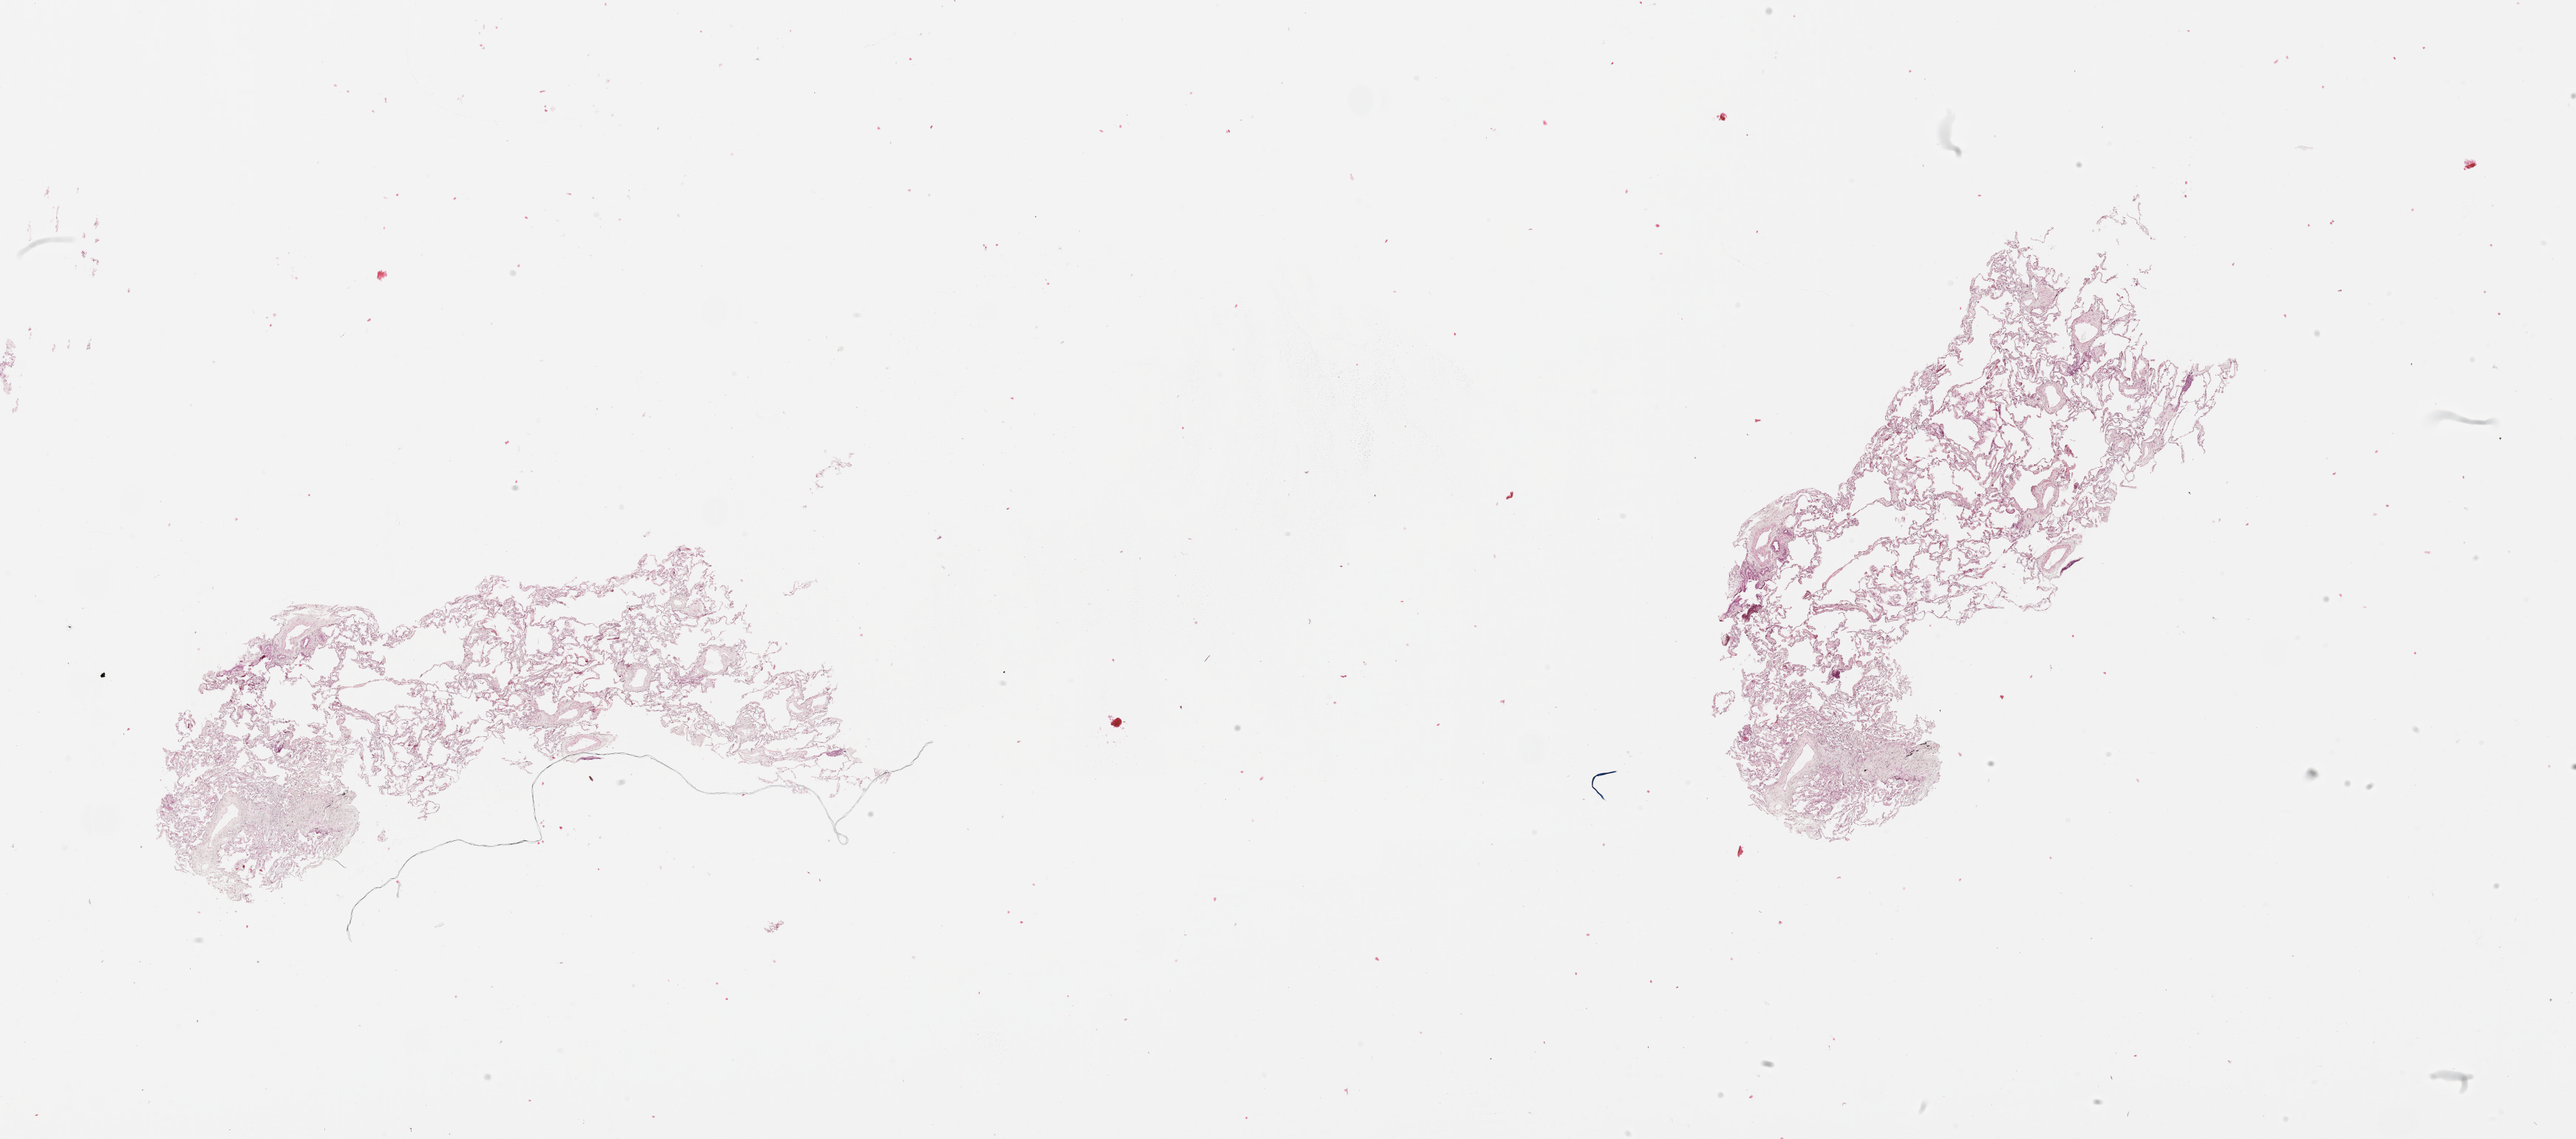
Digitized H&E tissue section (whole slide) — low-resolution overview of the scanned area, about 28.1 x 12.4 mm (from a 20x scan); lung, normal (non-tumour) tissue. 74-year-old female patient.
• this section: normal (non-tumour) tissue from the same patient
• patient diagnosis (cohort enrolment): squamous cell carcinoma (lung)